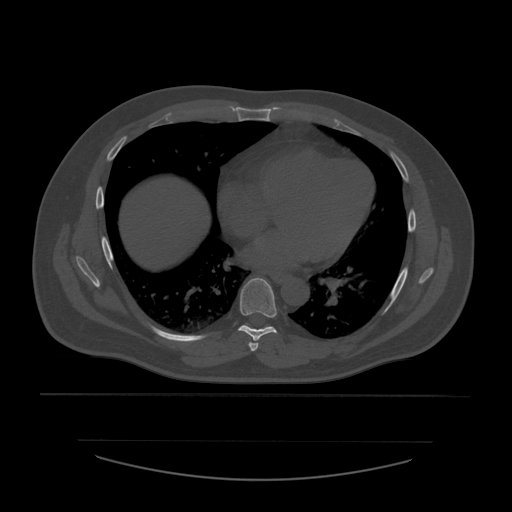
CT including the spine, one axial slice. Position 356 of 532 along the scan axis. Reconstruction kernel STANDARD. 120 kVp. Bone window (W 1800 / L 400 HU). 1.25 mm slice thickness. 512 × 512 image matrix, field of view 441 × 441 mm. Patient age 44 years. From the clinical record (not read from this slice): primary cancer: soft tissue sarcoma.
Annotated regions visible in this slice (semi-automatically segmented with operator editing):
- T6 vertebra: box from (x=249, y=342) to (x=259, y=353) px
- T7 vertebra: (x=238, y=278)–(x=277, y=344)